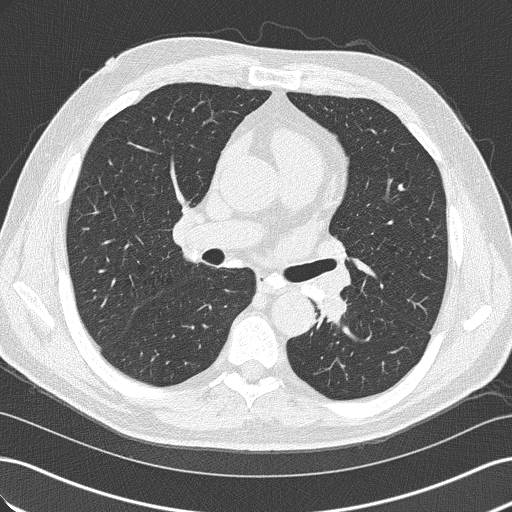
Axial slice from a low-dose chest CT screening exam. First (baseline) screen. Lung window (W 1500 / L -600 HU). 120 kVp. Slice 76 of 152 in the series. 512 × 512 image matrix, field of view 360 × 360 mm. Male, age 57 years at enrolment. Former smoker at enrolment.
- Expert reader's lesion annotation, box from (x=303, y=283) to (x=363, y=341) px.
- Screening reader's record for this exam: no non-calcified nodule ≥4 mm recorded.
- Later outcome: lung cancer diagnosed 363 days after this screen — squamous cell carcinoma, NOS, left lower lobe, moderately differentiated (G2), stage IIIB (AJCC 6th edition), 38 mm at pathology.